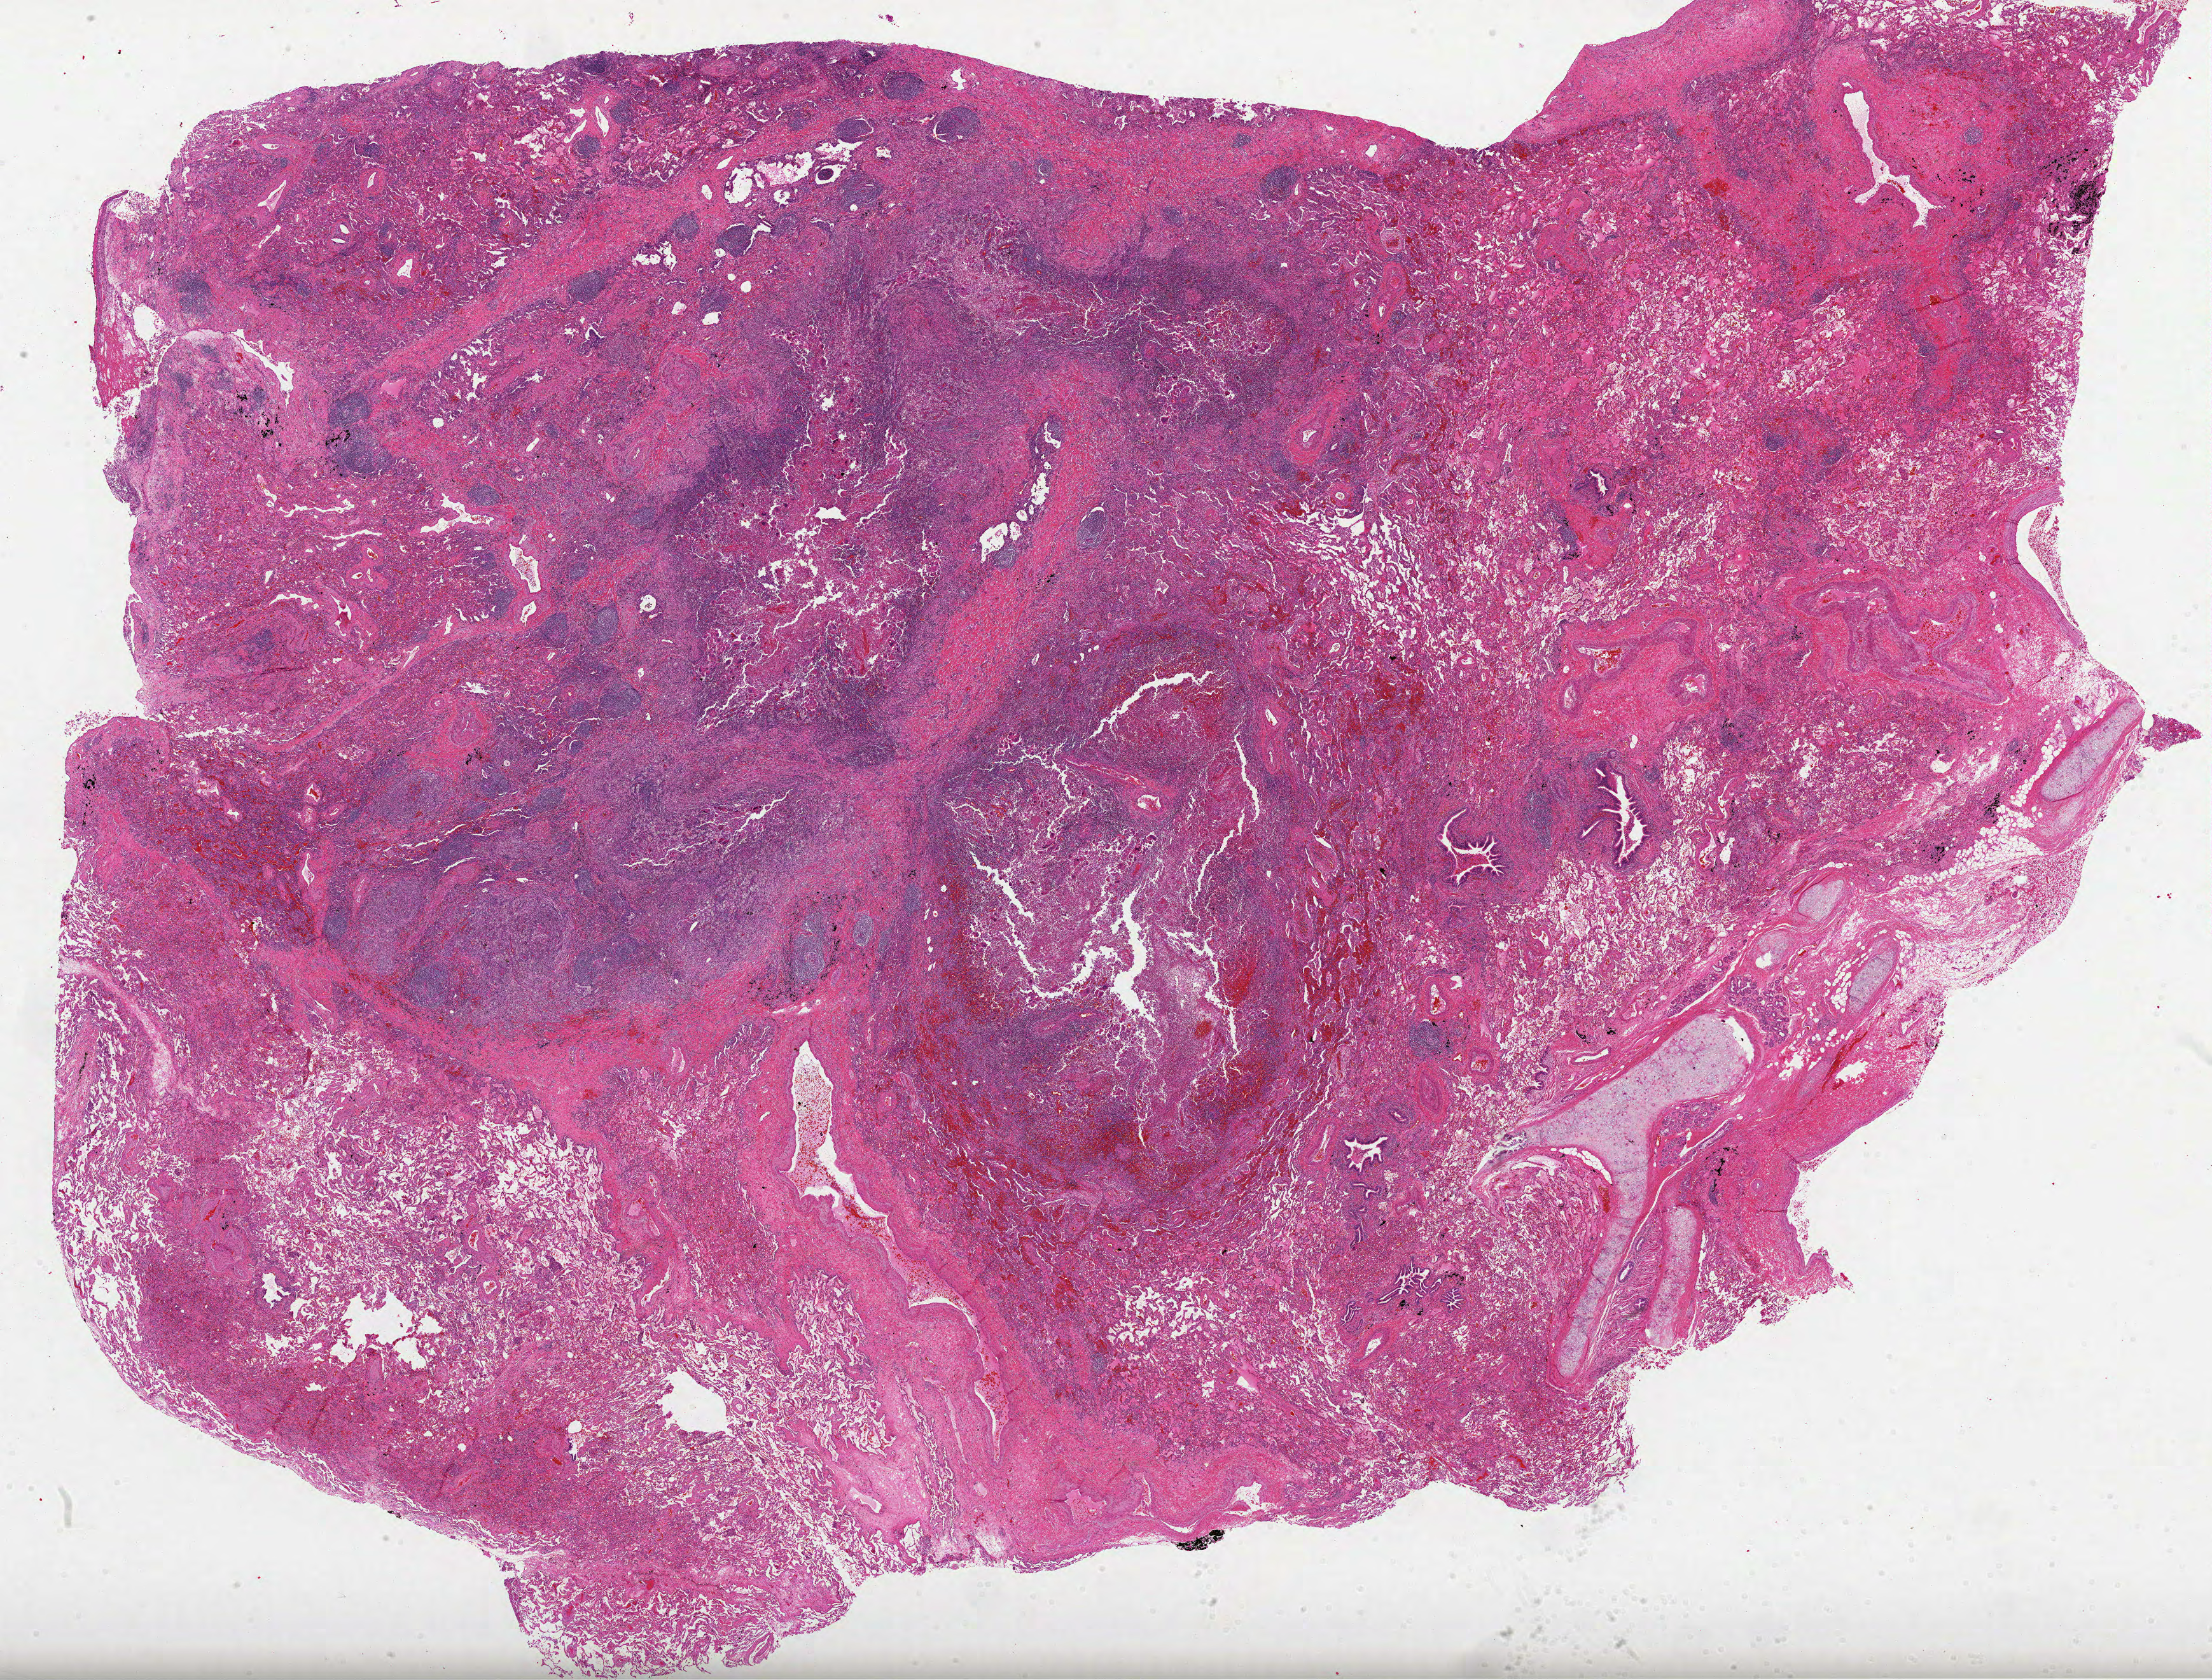
H&E whole-slide image — low-resolution overview of the scanned area, about 28.0 x 21.3 mm, FFPE section, sample: primary tumour, lung. Patient: male, age at initial diagnosis 73 years.
• AJCC pathologic stage: IA (5th edition)
• pathologic diagnosis: Squamous cell carcinoma, NOS (lower lobe, lung)